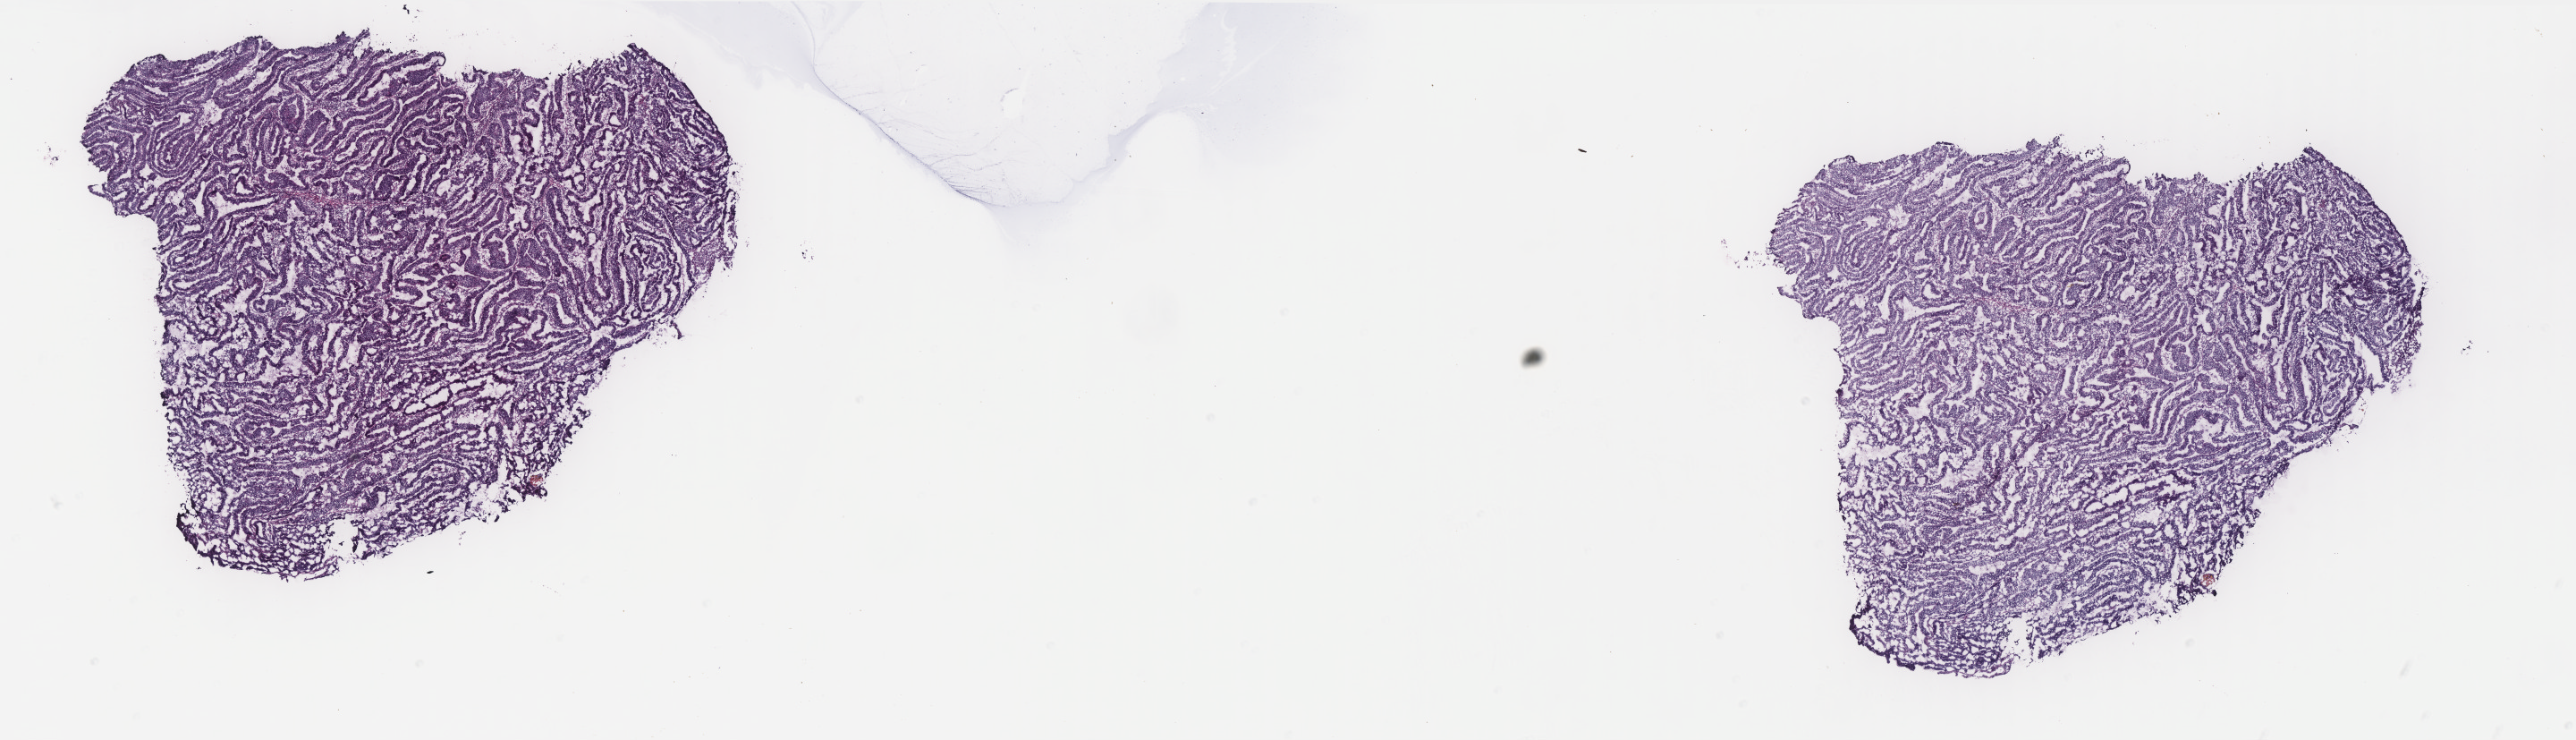
Digitized Hematoxylin and eosin (H&E) stained tissue section (whole slide) — low-resolution overview of the scanned area, about 23.1 x 6.6 mm (from a 40x scan). Frozen section from the top of the tissue portion. Uterus, primary tumour sample. Female patient; age at initial diagnosis 73 years. Histologic grade: G2 (moderately differentiated). Pathologist review of this section (percent, as recorded): tumour cells 89%, tumour nuclei 80%, normal cells 0%, stromal cells 10%, necrosis 1%. Inflammatory infiltration, as recorded: lymphocyte infiltration 8%, monocyte infiltration 0%, neutrophil infiltration 6%.
• lymph nodes positive (case pathology): 0 of 17 examined
• FIGO stage: IB
• histologic diagnosis: Endometrioid adenocarcinoma, NOS (endometrium)